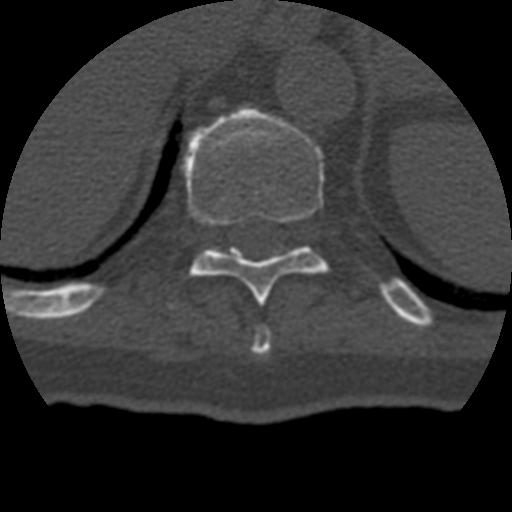
CT including the spine, one axial slice. Slice 215 of 399 in the series (ordered by position). Reconstruction kernel STANDARD. Bone window (W 1800 / L 400 HU). 512 × 512 image matrix, field of view 160 × 160 mm. Patient age 69 years. Case-level facts recorded for this patient, not image findings: primary cancer: prostate.
Outlined on this slice (semi-automatic segmentation, software-assisted and operator-edited):
- T10 vertebra: bounding box (x1, y1, x2, y2) in pixels: (183, 108, 329, 305)
- T11 vertebra: (208, 244, 211, 247)
- T9 vertebra: (252, 326, 272, 355)